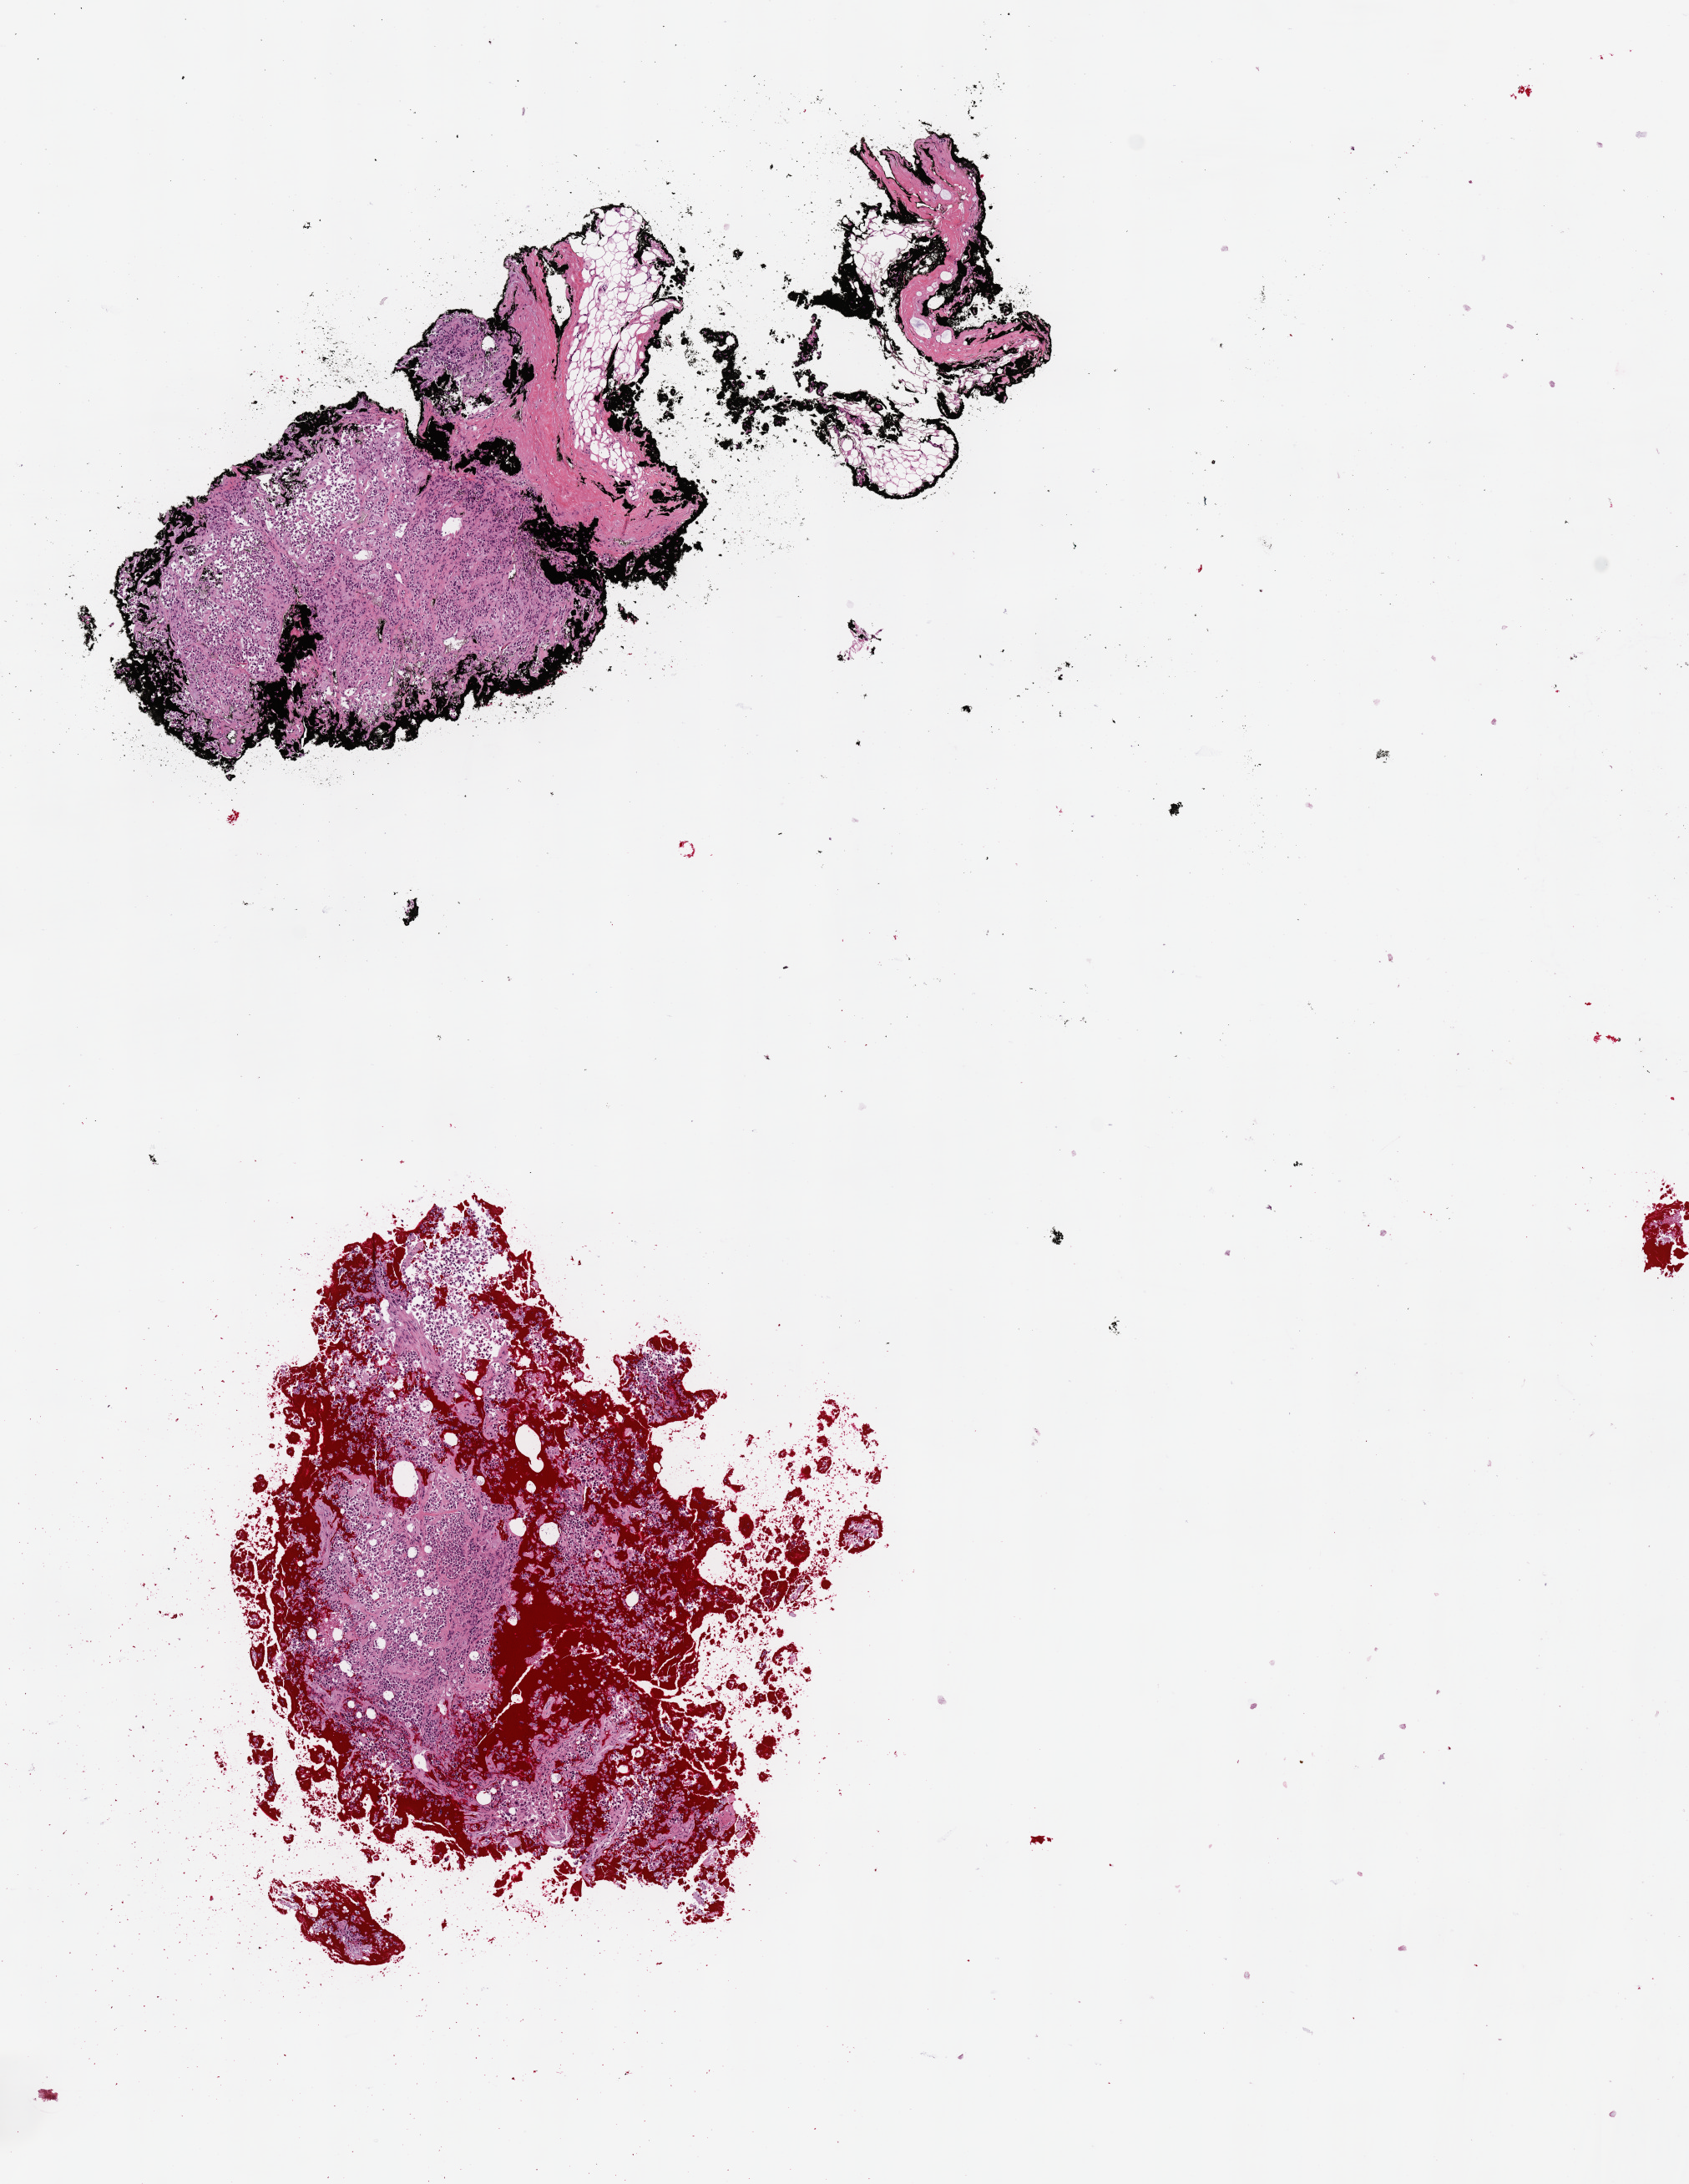
Digitized H&E tissue section (whole slide), shown as a low-resolution overview of the whole scanned area (about 8.2 x 10.6 mm, from a 20x scan). Frozen section from the top of the tissue portion. Sample: primary tumour, adrenal cortex. Female, age 55 years at initial diagnosis. Composition of this section per pathologist review: tumour cells 70%, tumour nuclei 80%, normal cells 0%, stromal cells 20%, necrosis 10%. Inflammatory infiltration, as recorded: lymphocyte infiltration 0%, monocyte infiltration 0%, neutrophil infiltration 0%.
Diagnosis: Adrenal cortical carcinoma. Laterality: right.